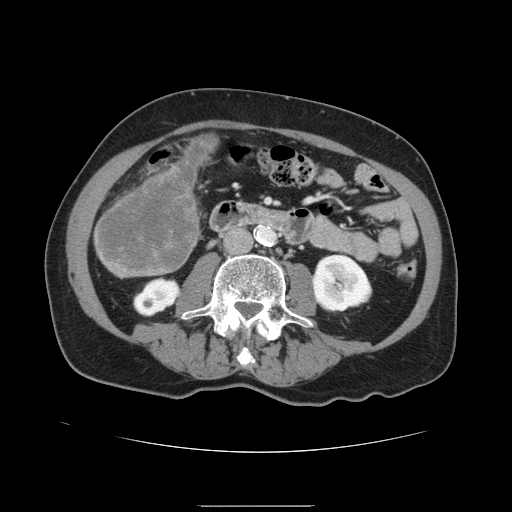
Contrast-enhanced abdominal CT, one axial slice; position 31 of 168 along the scan axis; 120 kVp; intravenous contrast given; soft-tissue window (W 400 / L 40 HU); 2.5 mm slice thickness; 512 × 512 image matrix, field of view 386 × 386 mm. Male patient, age 74 years. Case-level facts recorded for this patient, not image findings: diagnosis: colorectal cancer liver metastases, imaged before liver resection; multiple liver metastases: no; largest metastasis: 14.5 cm; chemotherapy before resection: no.
Annotated regions visible in this slice (expert manual segmentation):
- liver: box from (x=93, y=137) to (x=217, y=278) px
- liver metastasis: (x=97, y=141)–(x=214, y=274)